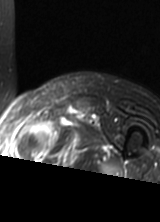
MRI of an extremity soft-tissue mass, one axial slice; T2-weighted fat-saturated; MR volume resampled by the dataset authors to the PET/CT grid (not the native acquisition matrix); 160 × 222 image matrix. Female patient. From the clinical record (not read from this slice): histological type: pleomorphic leiomyosarcoma; grade: high; site of the primary tumour: left thigh.
Annotated regions visible in this slice (expert contour drawn on MRI and transferred to this co-registered scan by the dataset authors):
- gross tumour volume including surrounding oedema: bounding box [x1, y1, x2, y2] px = [22, 123, 78, 158]